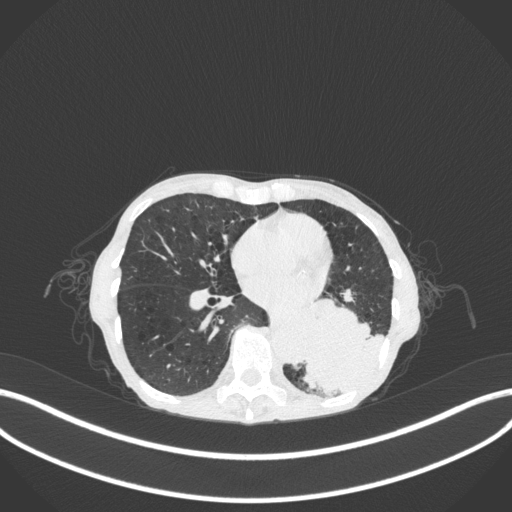
Chest CT, one axial slice. Slice 115 of 347 in the series (ordered by position). Reconstruction kernel B31f. Lung window (W 1500 / L -600 HU). 1 mm slice thickness. 512 × 512 image matrix. Patient: female, 70 years. From the clinical record (not read from this slice): clinical TNM (as recorded): T3 N0 M0.
Annotated regions visible in this slice (bounding box drawn by a radiologist):
- lung tumour (recorded histology: small cell carcinoma): bounding box [x1, y1, x2, y2] px = [304, 290, 387, 400]